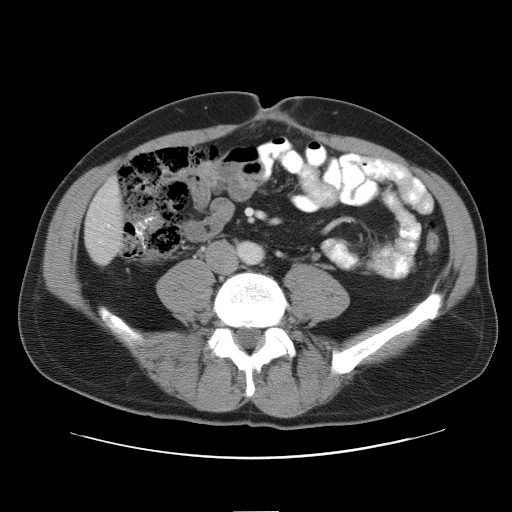
Contrast-enhanced abdominal CT, one axial slice; reconstruction kernel STANDARD; intravenous contrast given; soft-tissue window (W 400 / L 40 HU); 5 mm slice thickness; 512 × 512 image matrix. Male patient, age 70 years. From the clinical record (not read from this slice): diagnosis: colorectal cancer liver metastases, imaged before liver resection; multiple liver metastases: yes; largest metastasis: 4 cm; chemotherapy before resection: yes.
Outlined on this slice (manually delineated by an expert):
- liver: box from (x=86, y=181) to (x=124, y=264) px
- portal vein (with intrahepatic branches): (x=107, y=225)–(x=110, y=227)